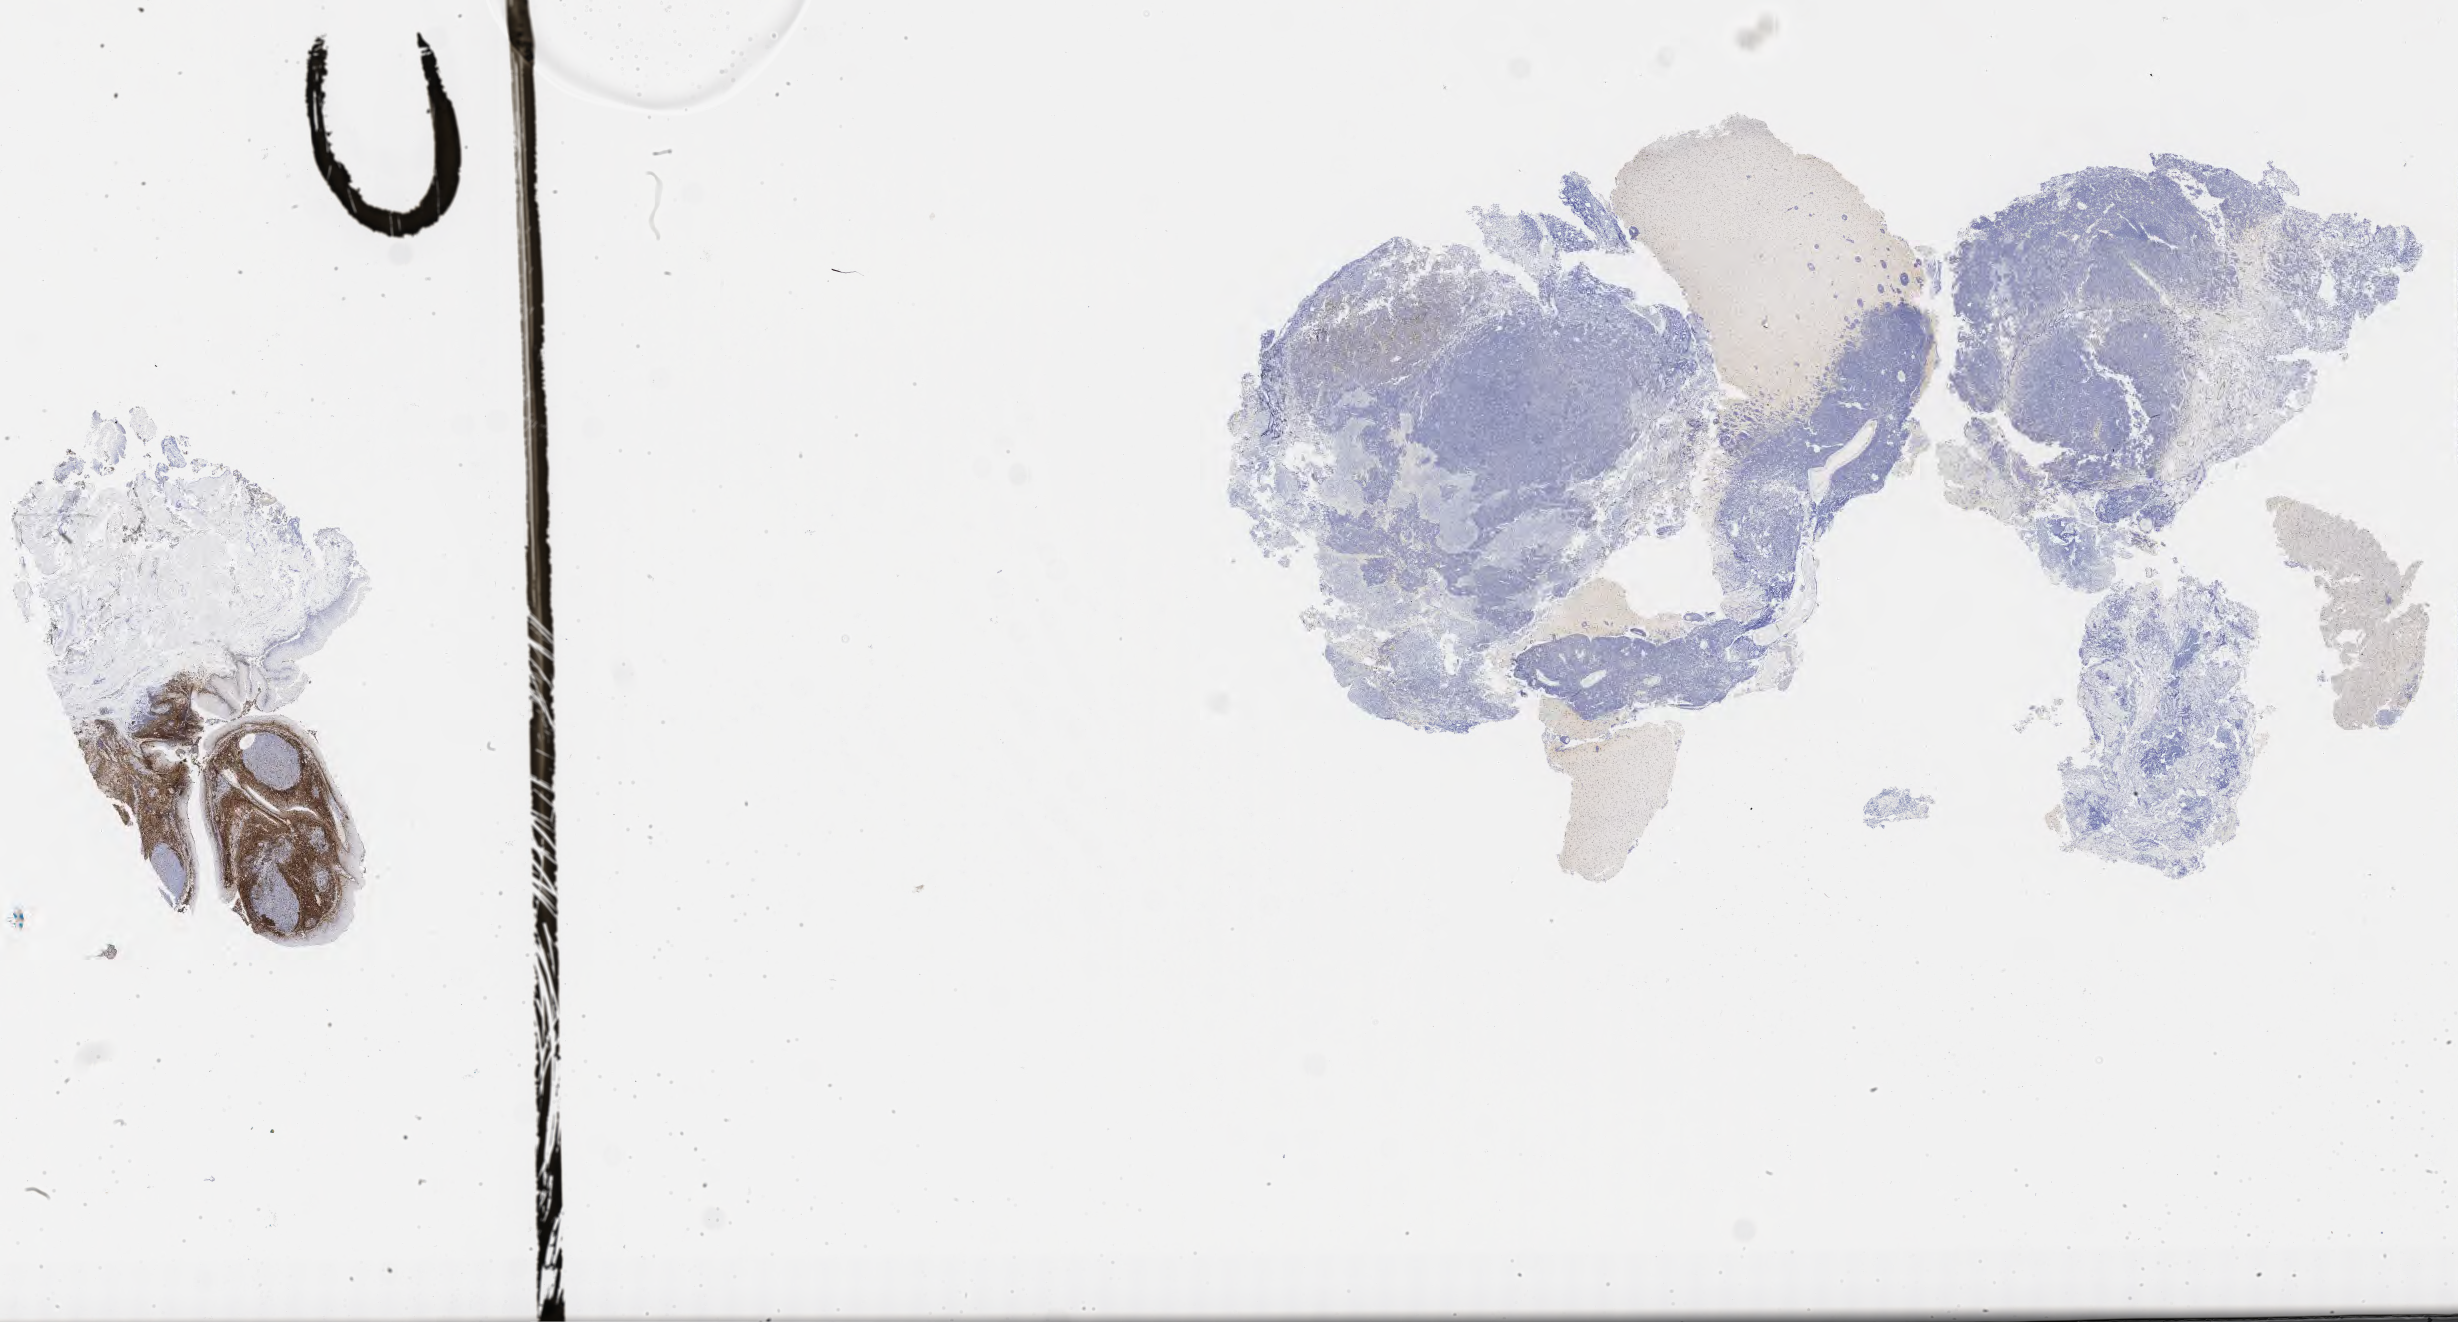
Whole-slide image, immunohistochemical stain for BCL2, a low-resolution overview of the entire scanned area, about 39.8 x 21.4 mm, specimen: tumor tissue. Female patient, aged 73.
Histologic diagnosis: Burkitt lymphoma, NOS.